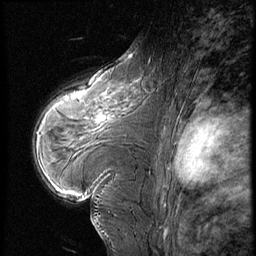
Breast MRI (dynamic contrast-enhanced), one sagittal slice. Position 40 of 60 along the scan axis. 3 images stored at this slice position (order not interpretable as contrast timing). 1.5 T. TE 4.2 ms, TR 8.9 ms. 2.5 mm slice thickness. 256 × 256 image matrix. Female patient, age 39 years. From the clinical record (not read from this slice): setting: breast cancer imaged before/during neoadjuvant chemotherapy; receptor status: HER2-positive.
Outlined on this slice (semi-automatically segmented with operator editing):
- analysis volume of interest (the breast-tissue region the enhancement analysis was run in; not a lesion): bounding box <72,79,141,135> (left, top, right, bottom; pixels)
- tumour enhancement mask (voxels above the 140 % enhancement threshold inside the analysis volume of interest): <96,117,105,122>